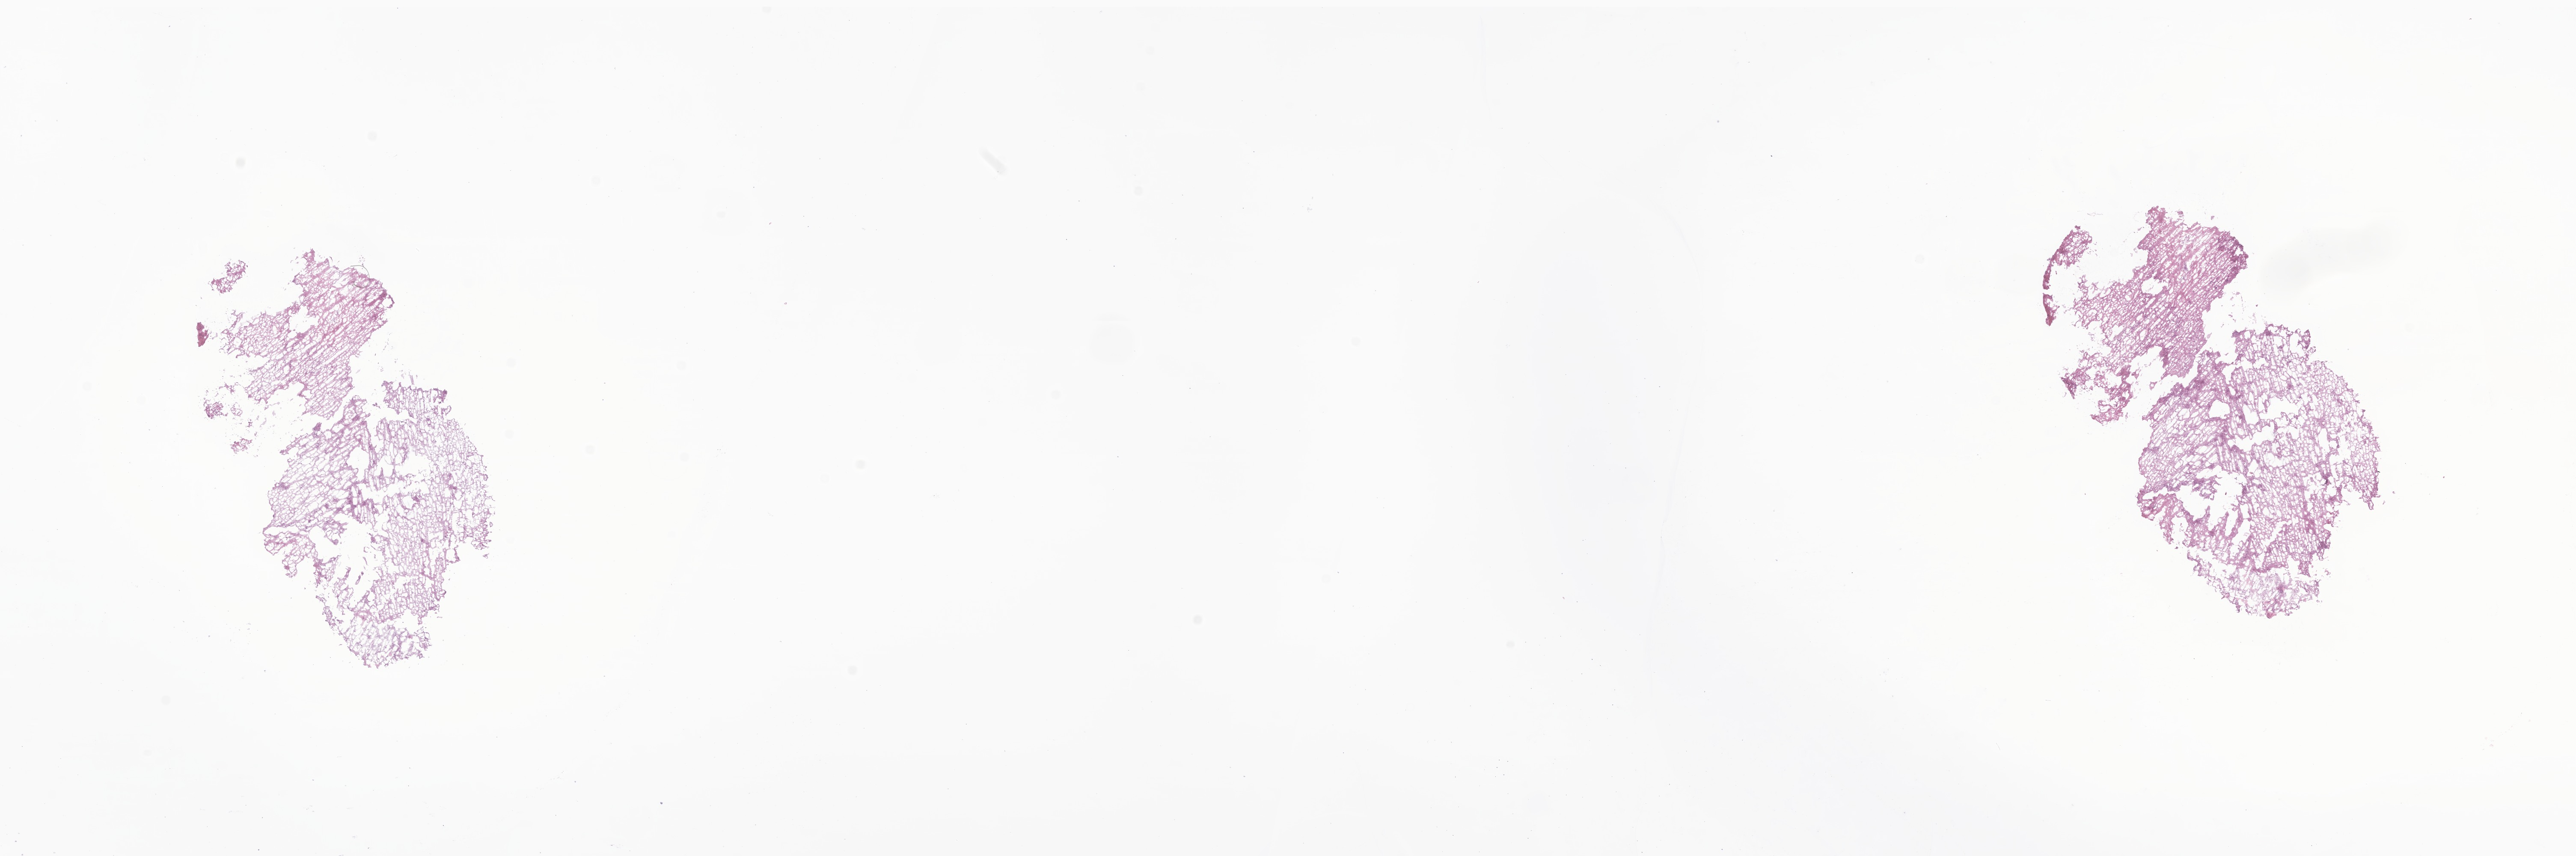
Hematoxylin and eosin (H&E) whole-slide image of tumor tissue from the brain — whole scanned area (about 25.4 x 8.4 mm) shown as a low-resolution overview; frozen section. Patient: male, age 262 months (21 years 10 months).
Recorded diagnosis: Oligoastrocytoma, NOS.